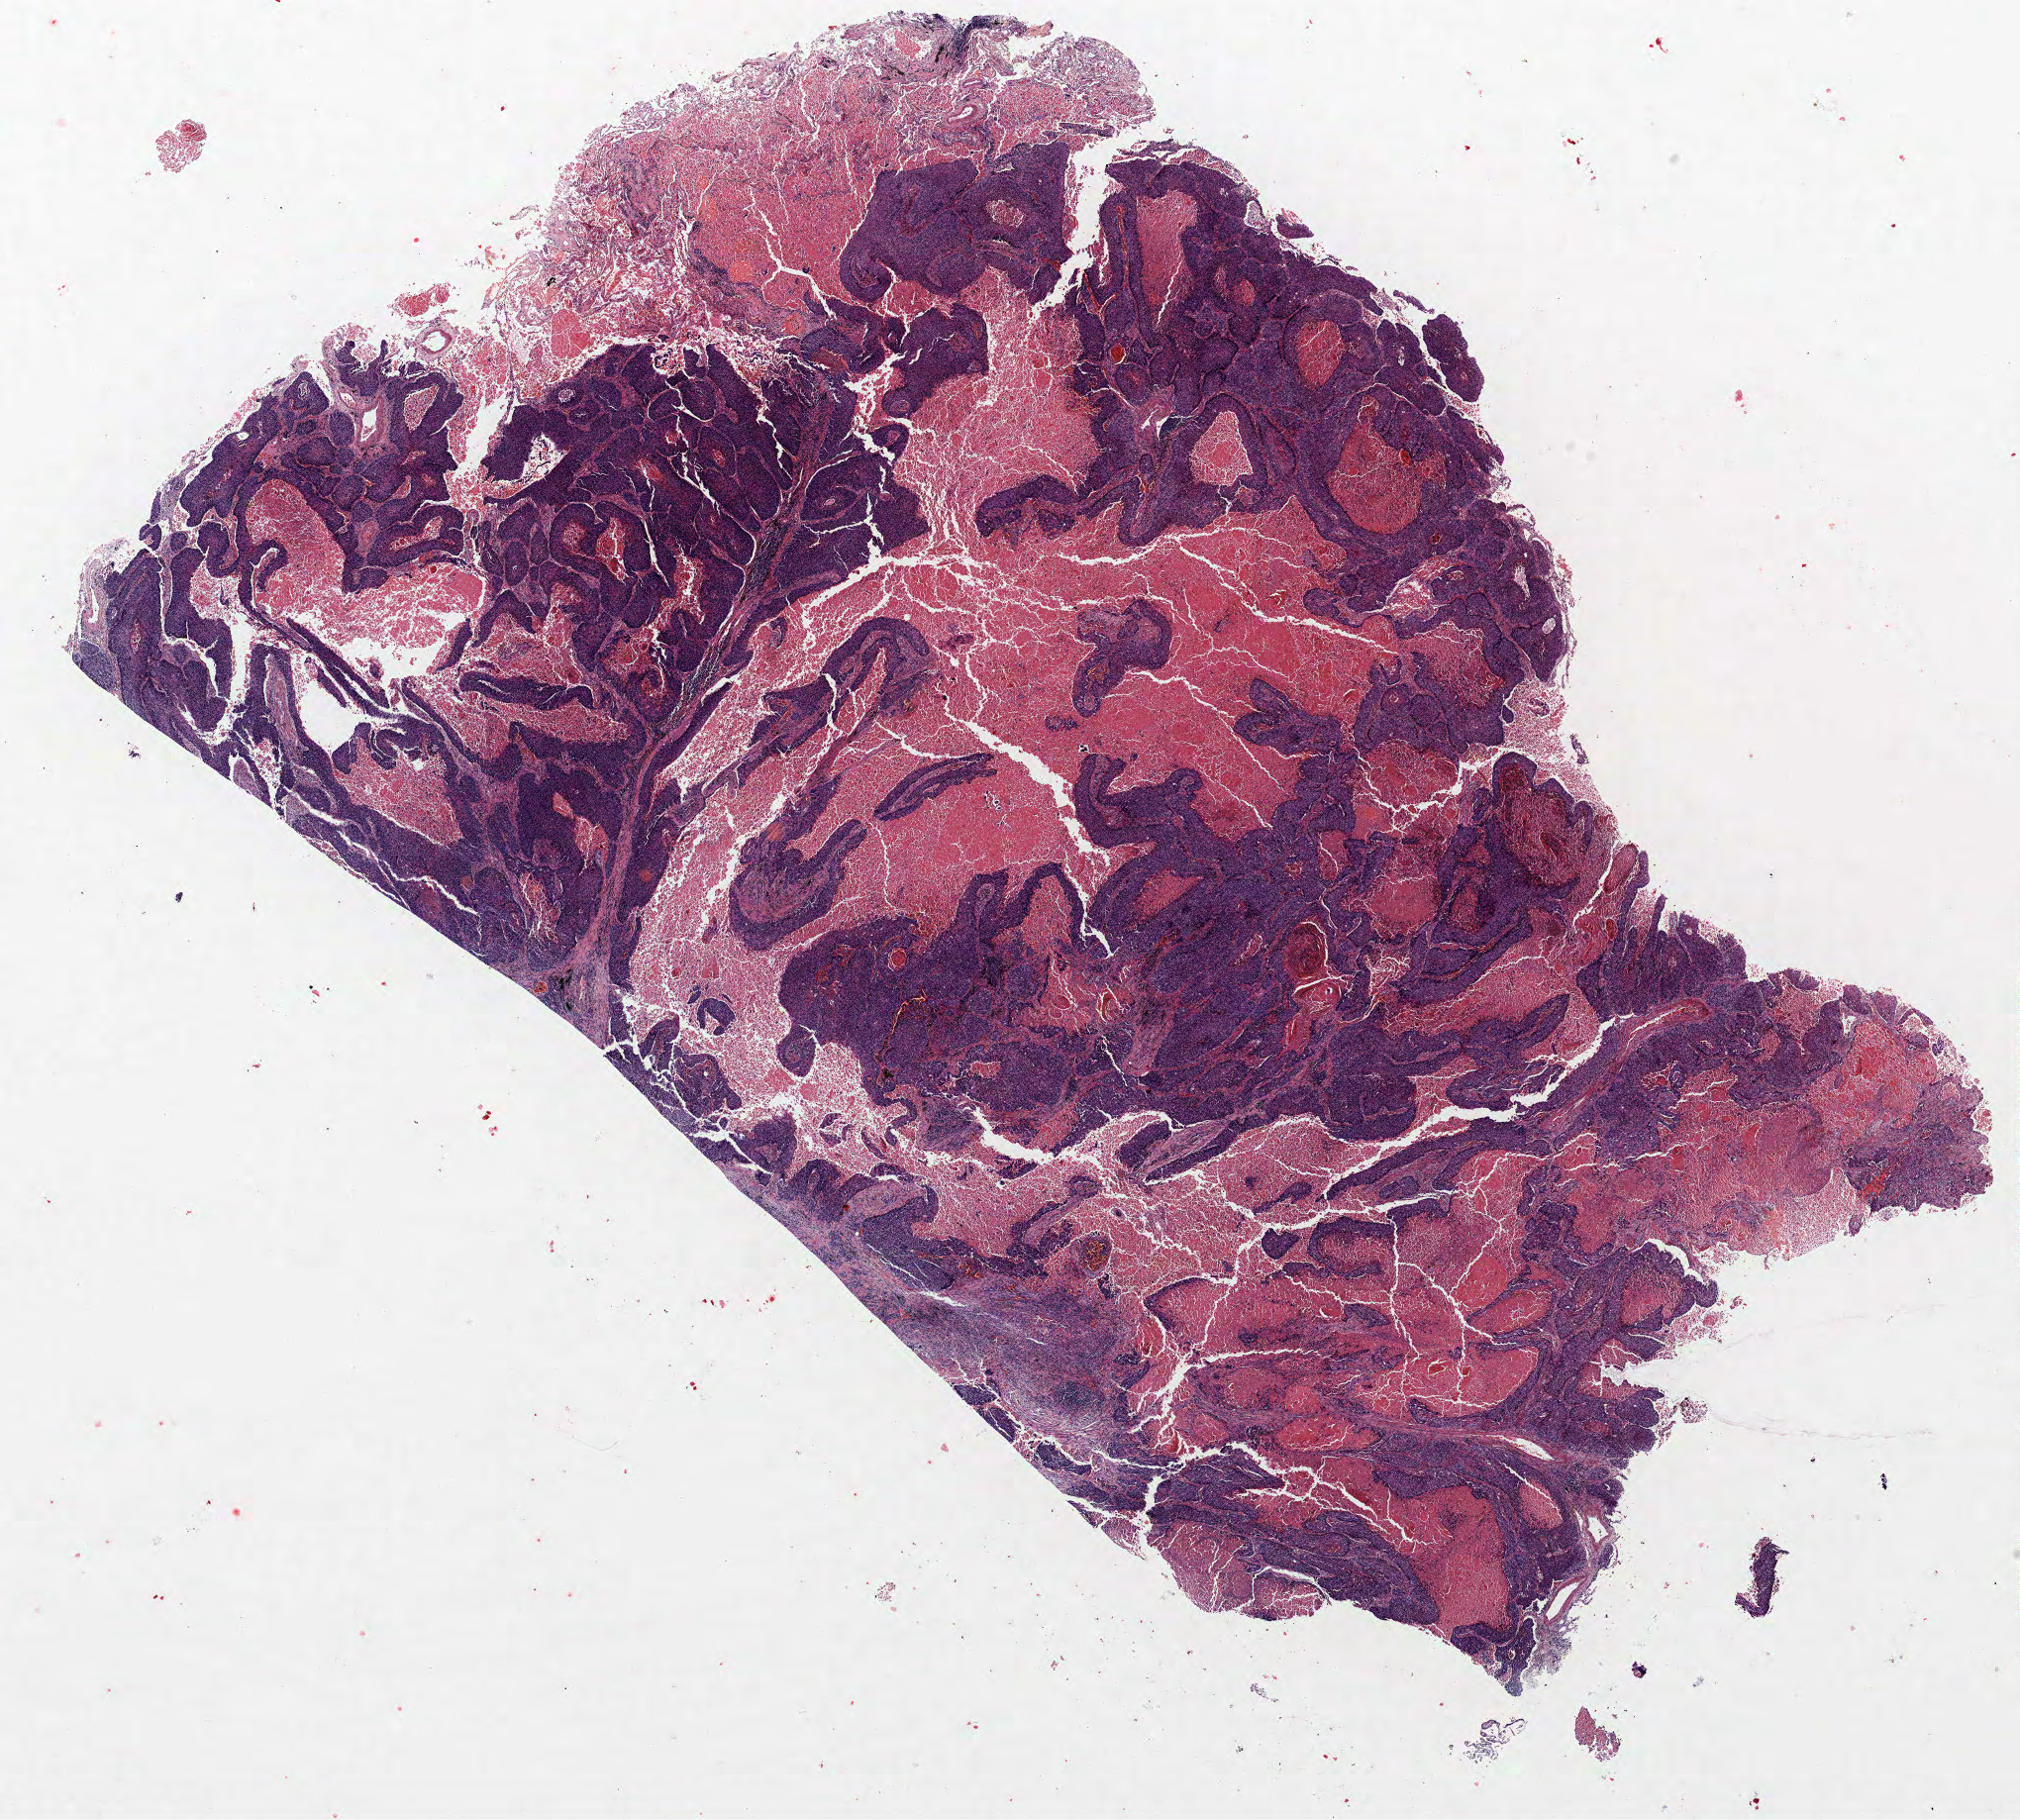
Whole-slide histology image, H&E-stained, whole scanned area (about 16.3 x 14.7 mm) shown as a low-resolution overview. Formalin-fixed paraffin-embedded (FFPE) section. Lung. Male, age 65 at enrolment. Former smoker at enrolment. Grade: moderately differentiated (G2).
ICD-O-3 topography: upper lobe of lung (C34.1). Participant's lung-cancer diagnosis: Squamous cell carcinoma, NOS. Stage (AJCC 6th edition): IA. Primary tumour location (clinical record): right upper lobe. Tumour size (pathology): 16 mm.